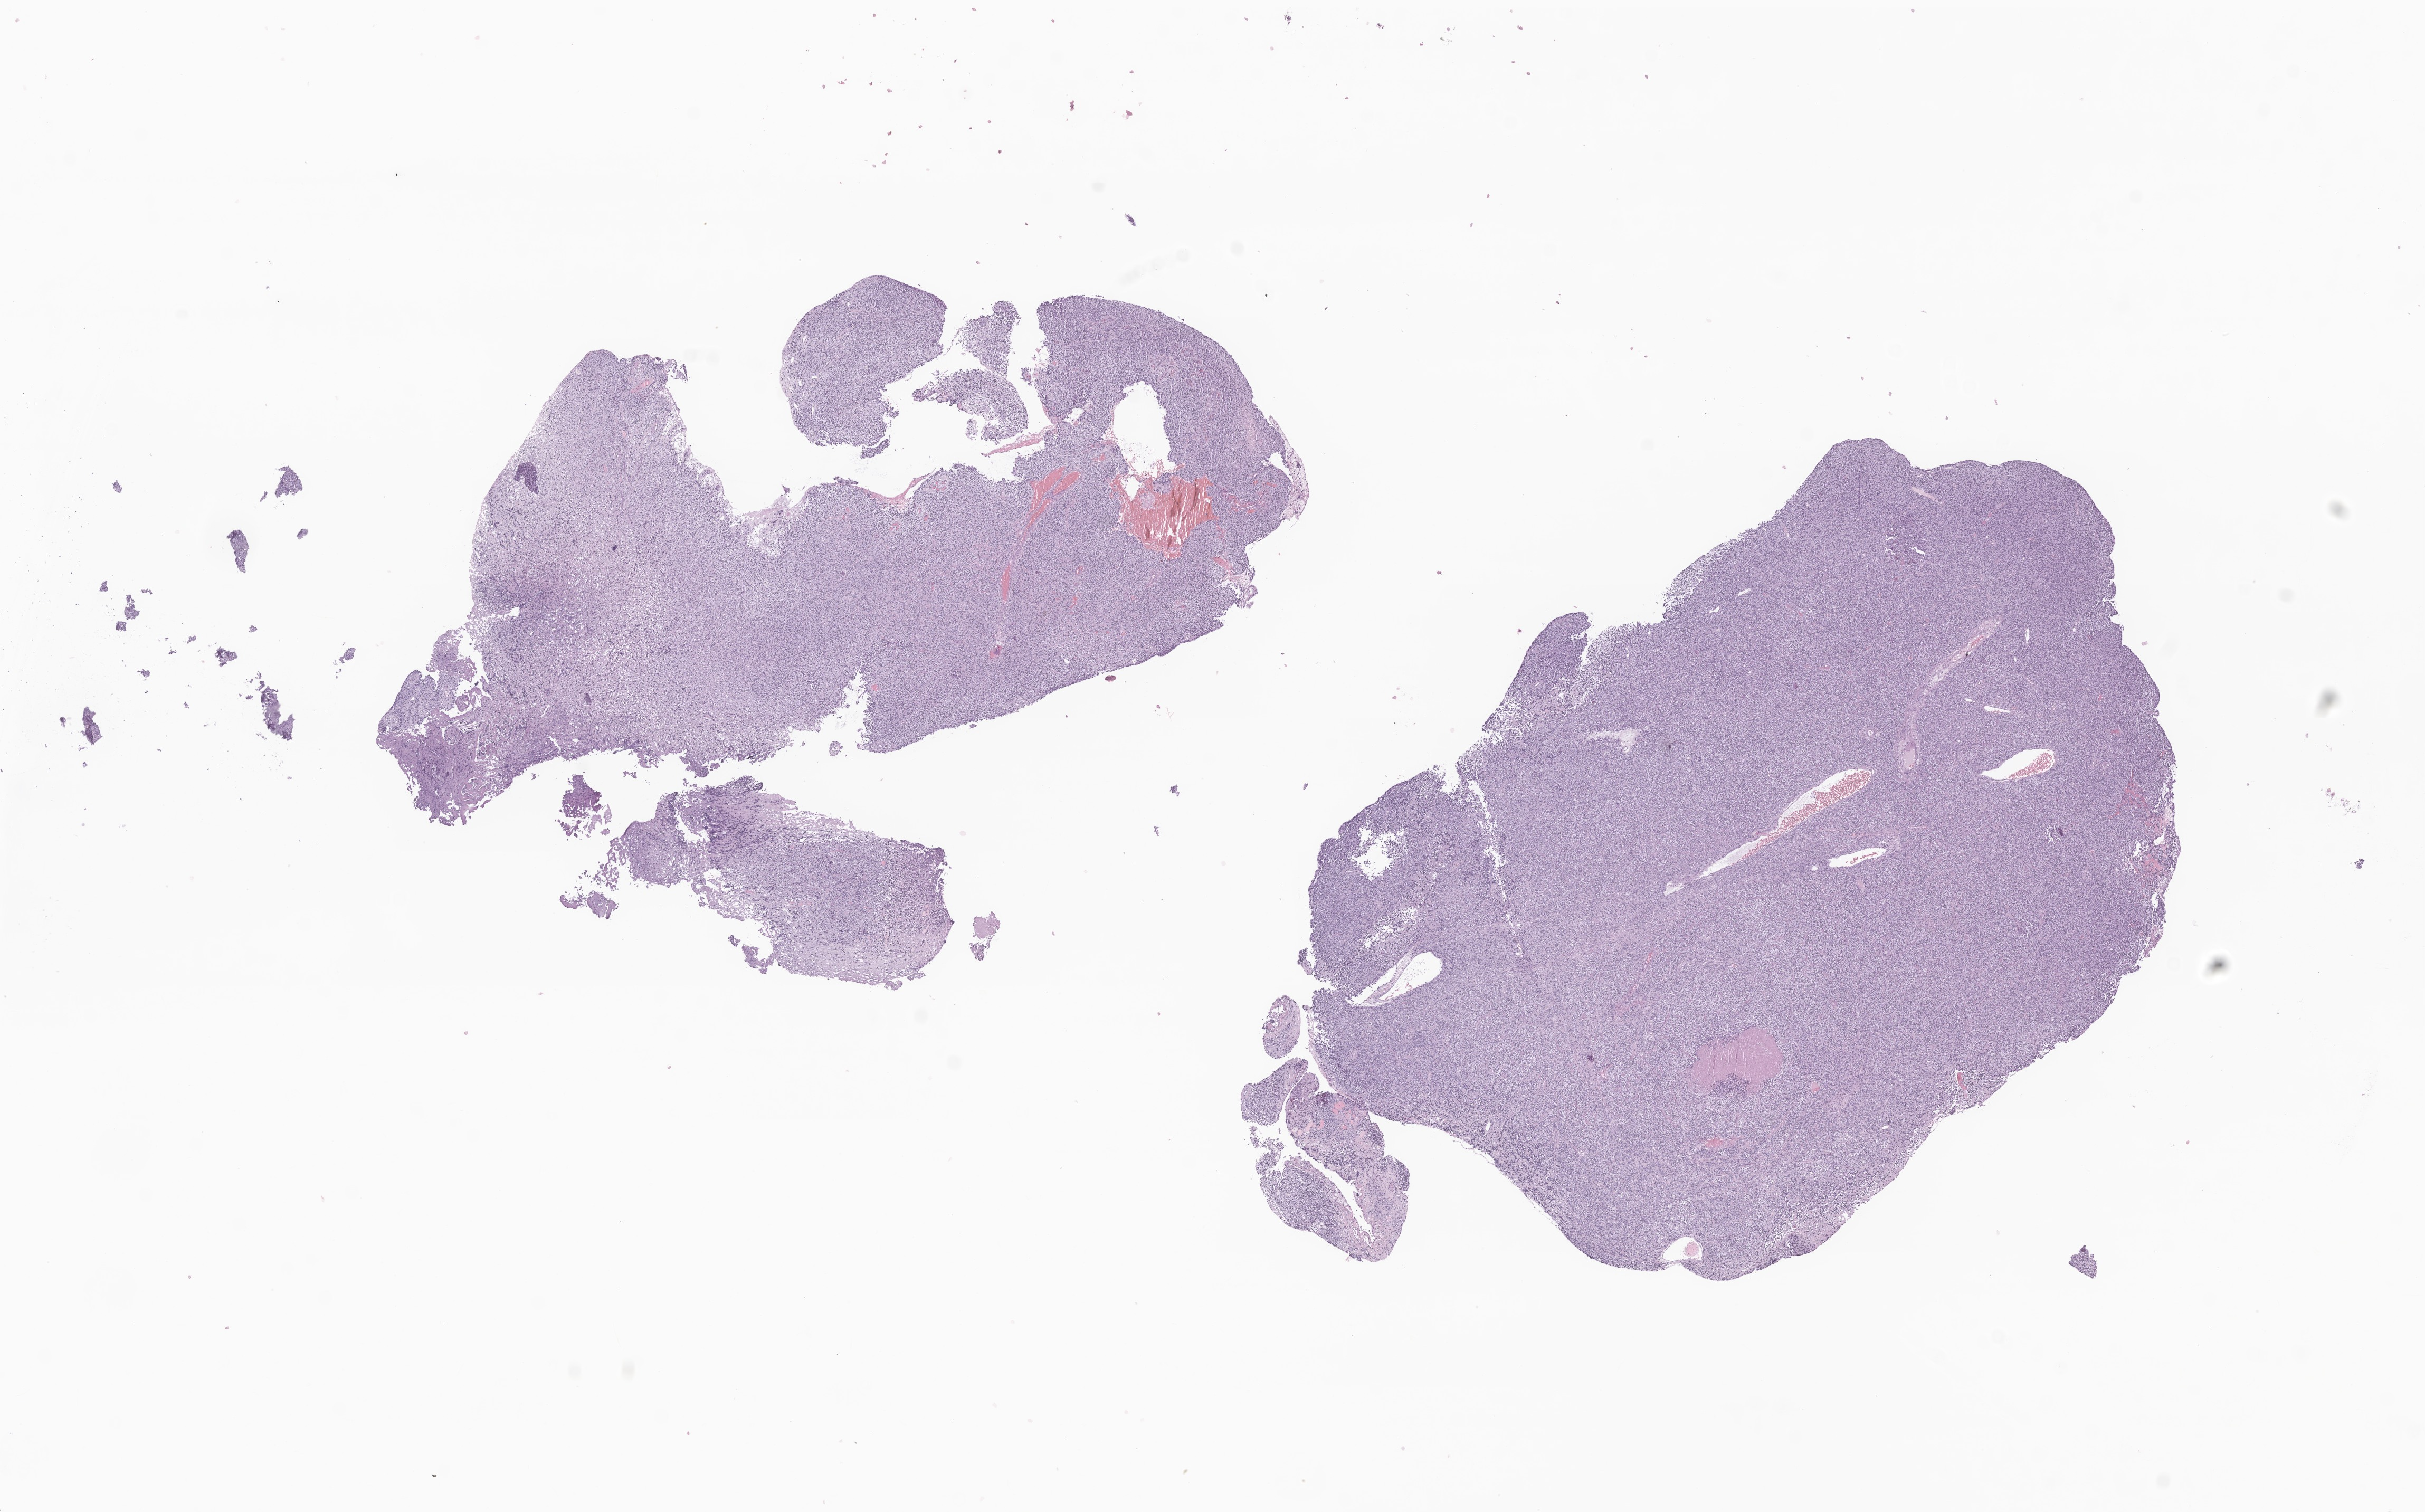
Whole-slide image, hematoxylin and eosin (H&E) stain of tumor tissue from the brain stem — a low-resolution overview of the entire scanned area, about 19.4 x 12.1 mm. Formalin-fixed paraffin-embedded section. Patient female; age 36 months.
* diagnosis: Astroblastoma